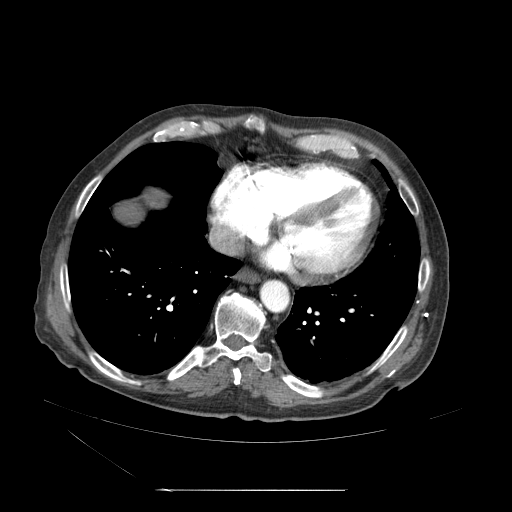
Contrast-enhanced abdominal CT (liver protocol), one axial slice; 120 kVp; soft-tissue window (W 400 / L 40 HU); 2.5 mm slice thickness; 512 × 512 image matrix, field of view 440 × 440 mm. Case-level facts recorded for this patient, not image findings: diagnosis: hepatocellular carcinoma (patient treated with transarterial chemoembolisation; whether this scan precedes or follows treatment is not stated here); TNM stage (as recorded): Stage-II; Child-Pugh class: A.
Outlined on this slice (semi-automatic segmentation, software-assisted and operator-edited):
- abdominal aorta: bounding box (x1, y1, x2, y2) in pixels: (260, 278, 289, 313)
- liver parenchyma outside the tumour (the mass and vessels are separate outlines, so this box may not span the whole liver): (156, 199, 173, 215)